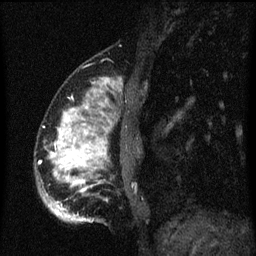
Breast MRI (dynamic contrast-enhanced), one sagittal slice. Slice 17 of 60 in the series (ordered by position). Dynamic contrast-enhanced series, image 2 of 3 at this slice position (ordered by acquisition). 1.5 T. TE 4.2 ms, TR 8.4 ms. 2 mm slice thickness. 256 × 256 image matrix, field of view 180 × 180 mm. Female patient, age 34 years. From the clinical record (not read from this slice): setting: breast cancer imaged before/during neoadjuvant chemotherapy; receptor status: HR-positive, HER2-negative.
Structures marked on this image (semi-automatic segmentation, software-assisted and operator-edited):
- analysis volume of interest (the breast-tissue region the enhancement analysis was run in; not a lesion): bounding box (x1, y1, x2, y2) in pixels: (36, 70, 143, 225)
- tumour enhancement mask (voxels above the 70 % enhancement threshold inside the analysis volume of interest): (50, 78, 109, 223)